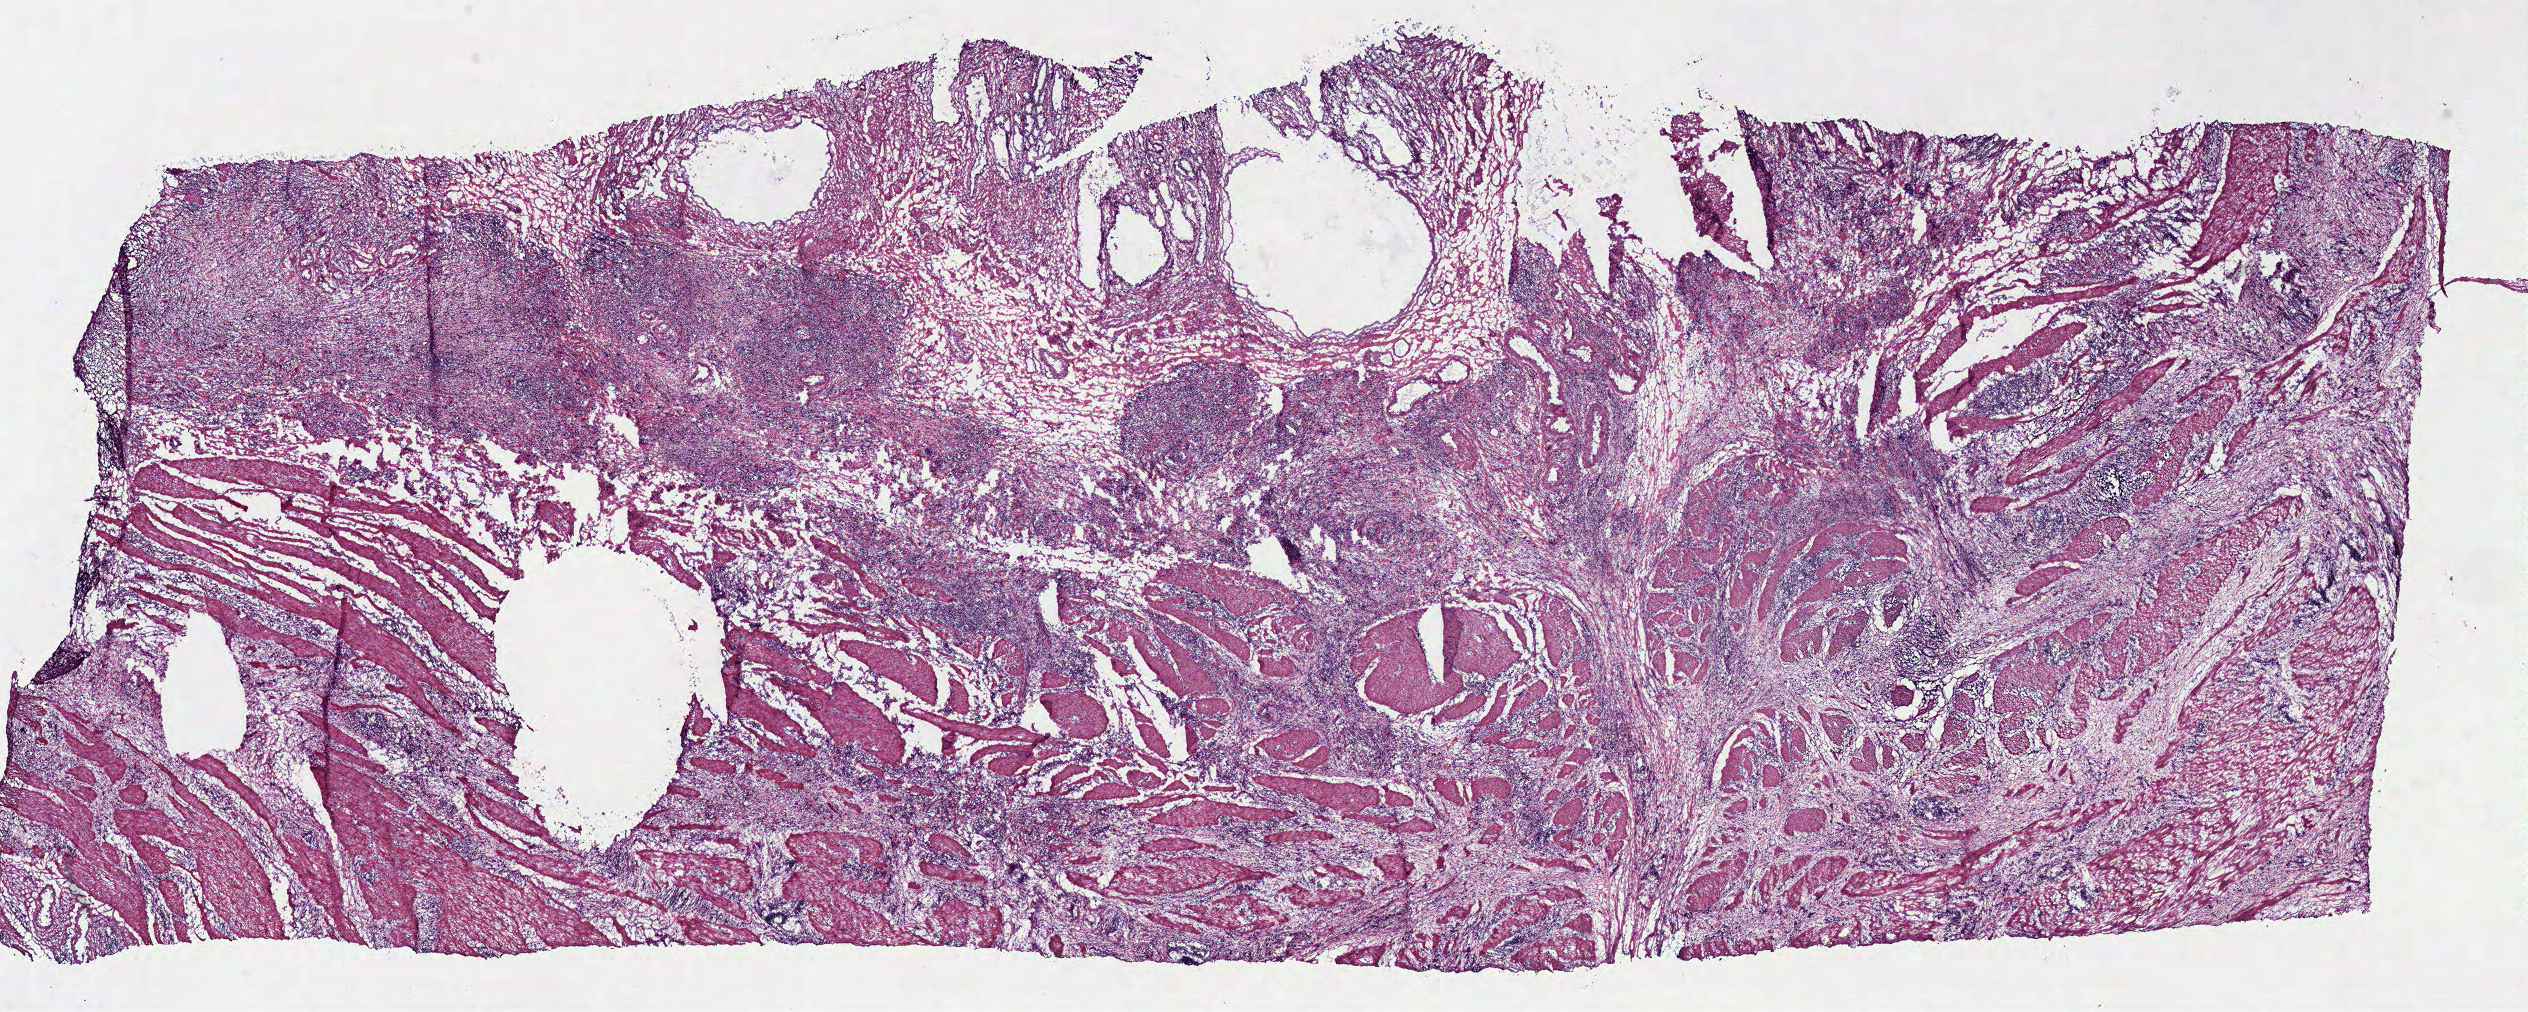
Hematoxylin and eosin (H&E) stained whole-slide image, low-resolution overview of the scanned area, about 19.9 x 8.0 mm, frozen section from the bottom of the tissue portion, stomach, primary tumour sample. Female, age 78 years at initial diagnosis. Histologic grade: G3 (poorly differentiated). Pathologist review of this section (percent, as recorded): tumour cells 45%, tumour nuclei 50%, normal cells 40%, stromal cells 15%, necrosis 0%.
AJCC pathologic stage: II. TNM: T3 N0 M0. Histologic diagnosis: Adenocarcinoma, NOS.